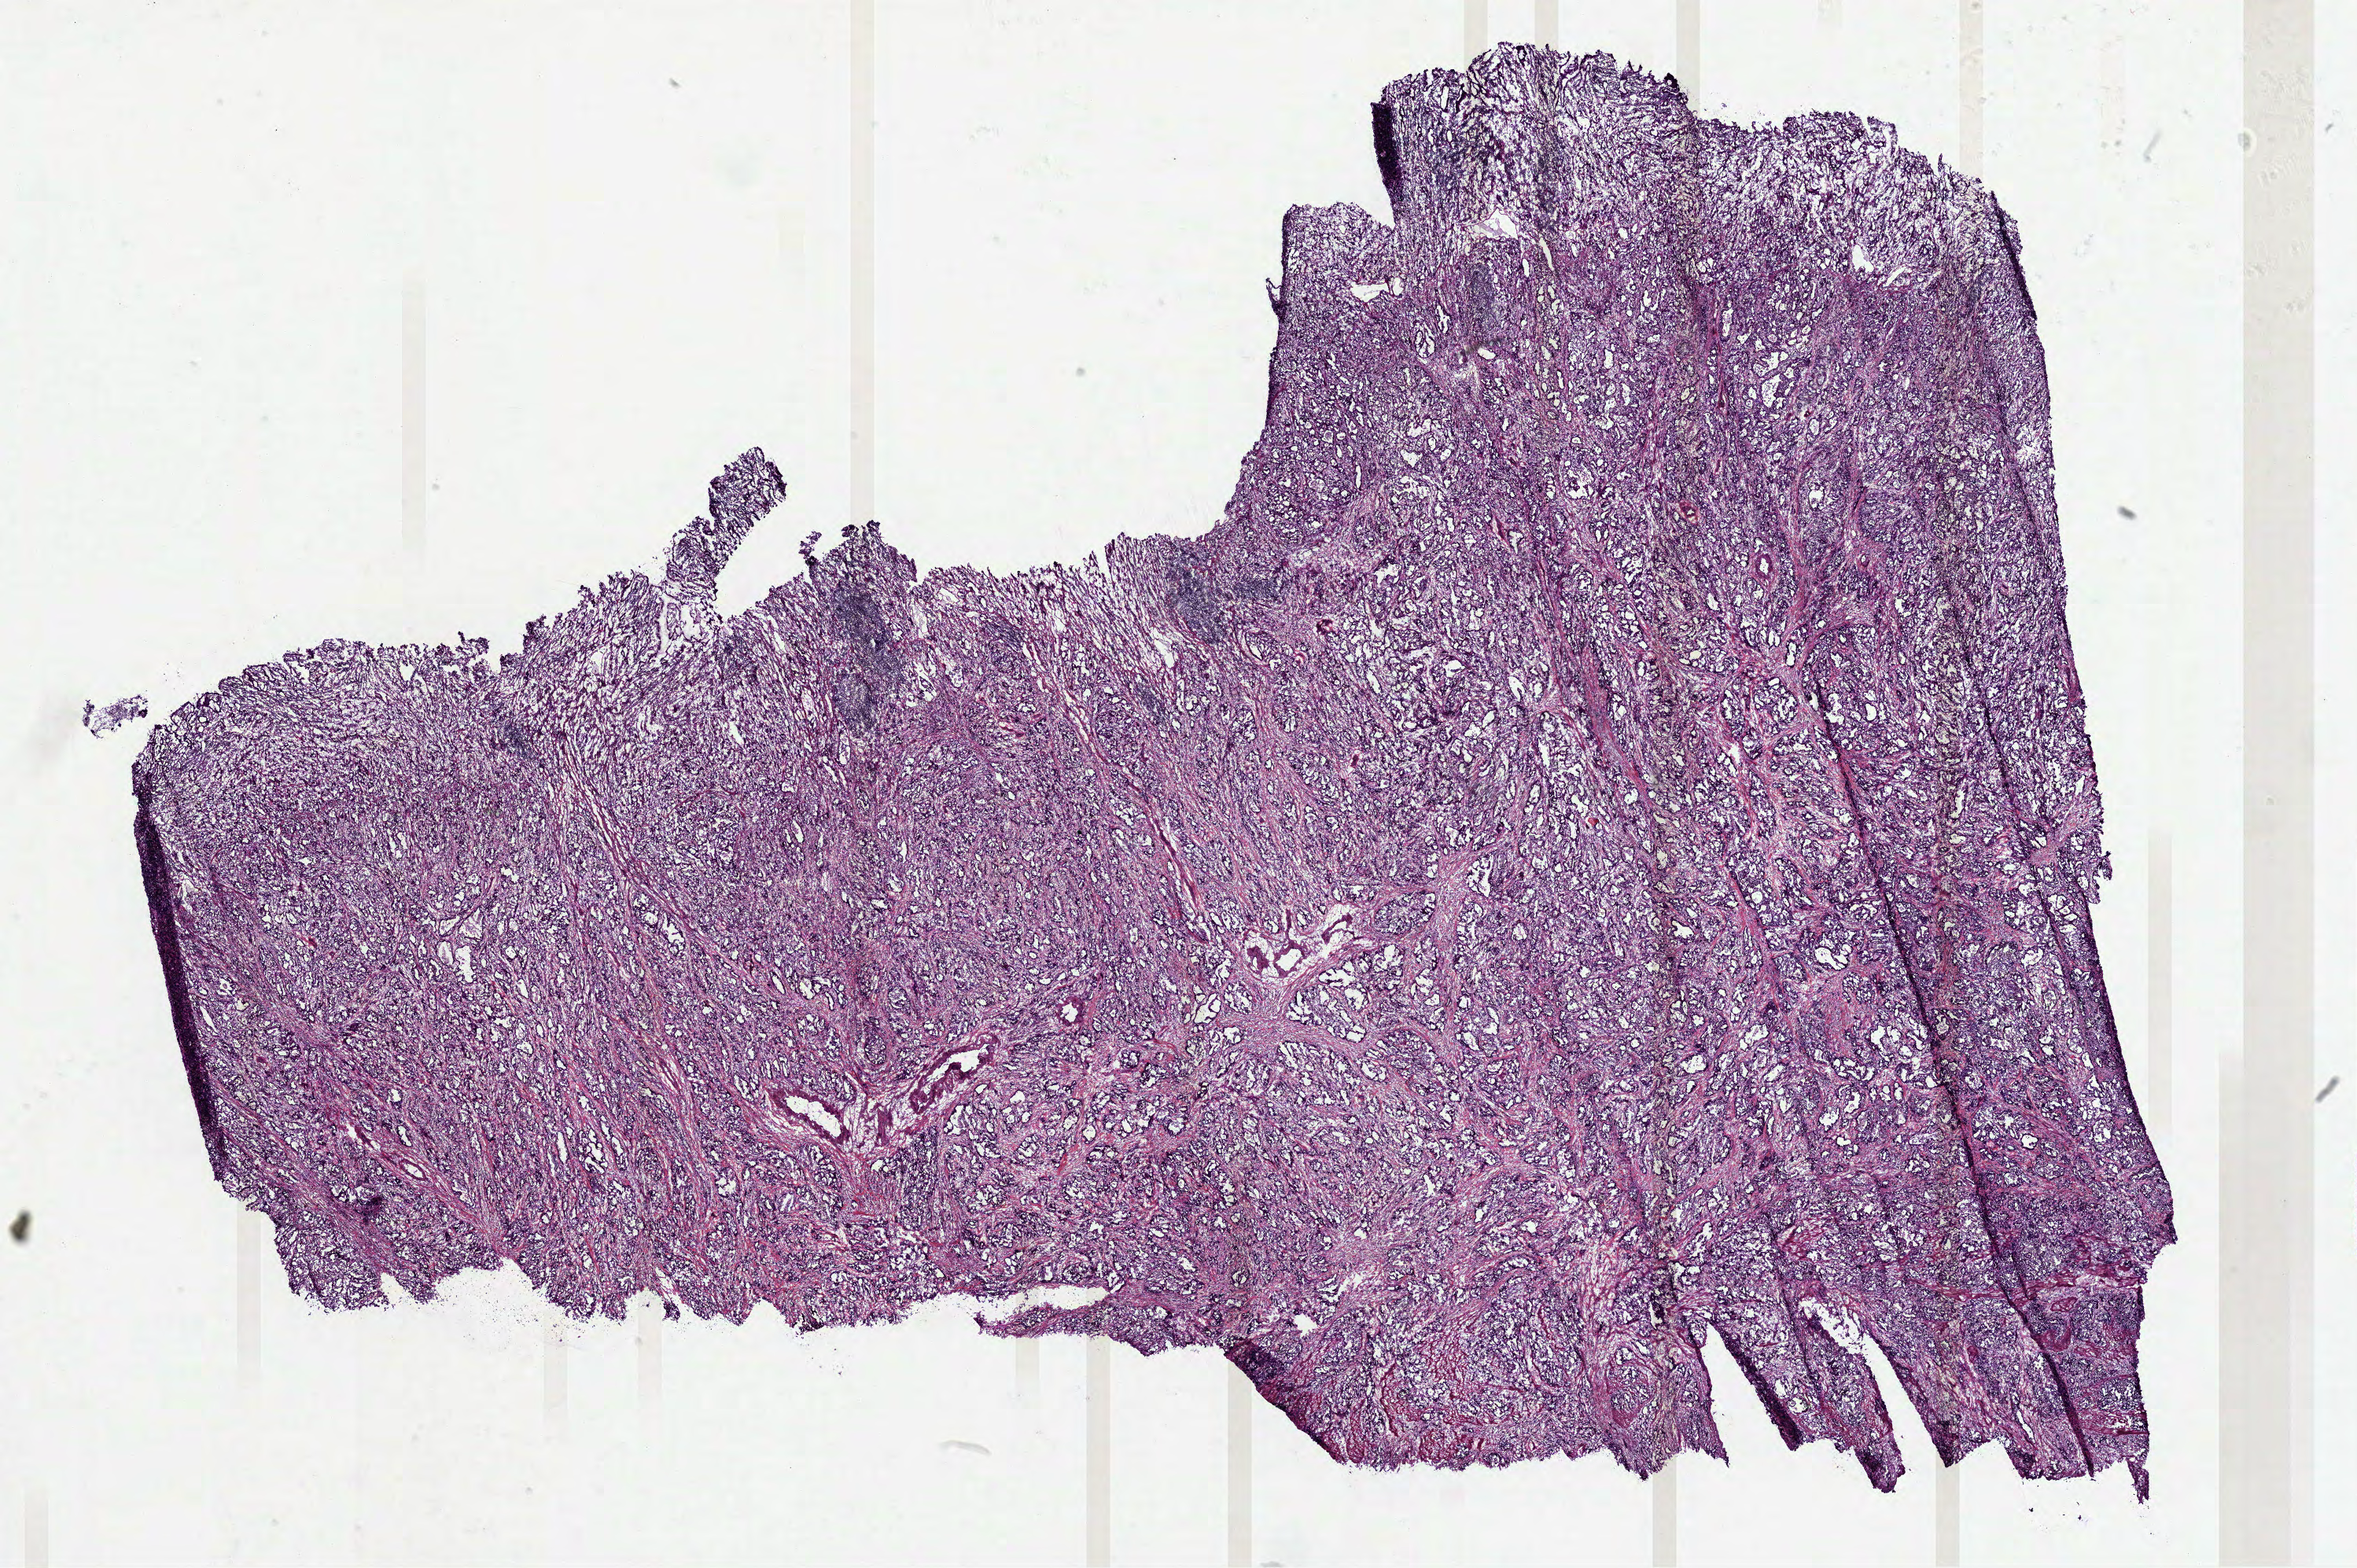
Hematoxylin and eosin (H&E) stained whole-slide image — low-resolution overview of the scanned area, about 24.2 x 16.1 mm, frozen section from the bottom of the tissue portion, sample: primary tumour, stomach. Patient: female, age at initial diagnosis 58 years. Histologic grade: G3 (poorly differentiated). Pathologist review of this section (percent, as recorded): tumour cells 80%, tumour nuclei 80%, normal cells 0%, stromal cells 15%, necrosis 5%.
AJCC pathologic stage: IIIC (7th edition). Lymph nodes positive (case pathology): 6 of 7 examined. Histologic diagnosis: Adenocarcinoma, intestinal type (body of stomach).